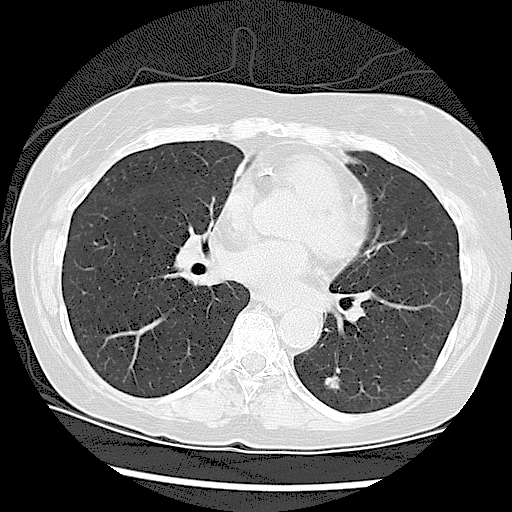
Chest CT (low-dose screening protocol), one axial image, second screening round (one year after baseline), lung window (W 1500 / L -600 HU), slice 60 of 108 in the series. Female, age 61 years at enrolment. Current smoker at enrolment.
• Expert reader's lesion annotation, bounding box <305,358,356,406> (left, top, right, bottom; pixels).
• The screening reader recorded 2 non-calcified nodules or masses ≥4 mm on this exam; which of them this box marks is not recorded.
• Official screen result: positive, other.
• Lung cancer was diagnosed 178 days after this screen: adenocarcinoma, NOS, left lower lobe, moderately differentiated (G2), stage IA (AJCC 6th edition), 18 mm at pathology.